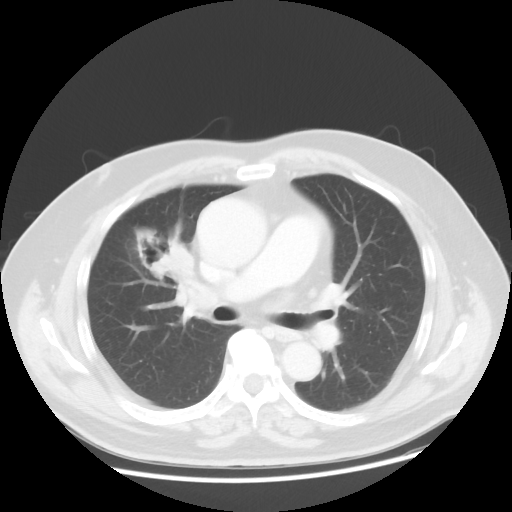
Chest CT, one axial slice; slice 27 of 48 in the series (ordered by position); reconstruction kernel STANDARD; lung window (W 1500 / L -600 HU); 5 mm slice thickness; 512 × 512 image matrix, field of view 392 × 392 mm. Patient: male, 60 years. Case-level facts recorded for this patient, not image findings: clinical TNM (as recorded): T2 N3 M0; histopathological grade: G2-3.
Structures marked on this image (bounding box drawn by a radiologist):
- lung tumour (recorded histology: adenocarcinoma): bounding box [x1, y1, x2, y2] px = [125, 215, 197, 298]